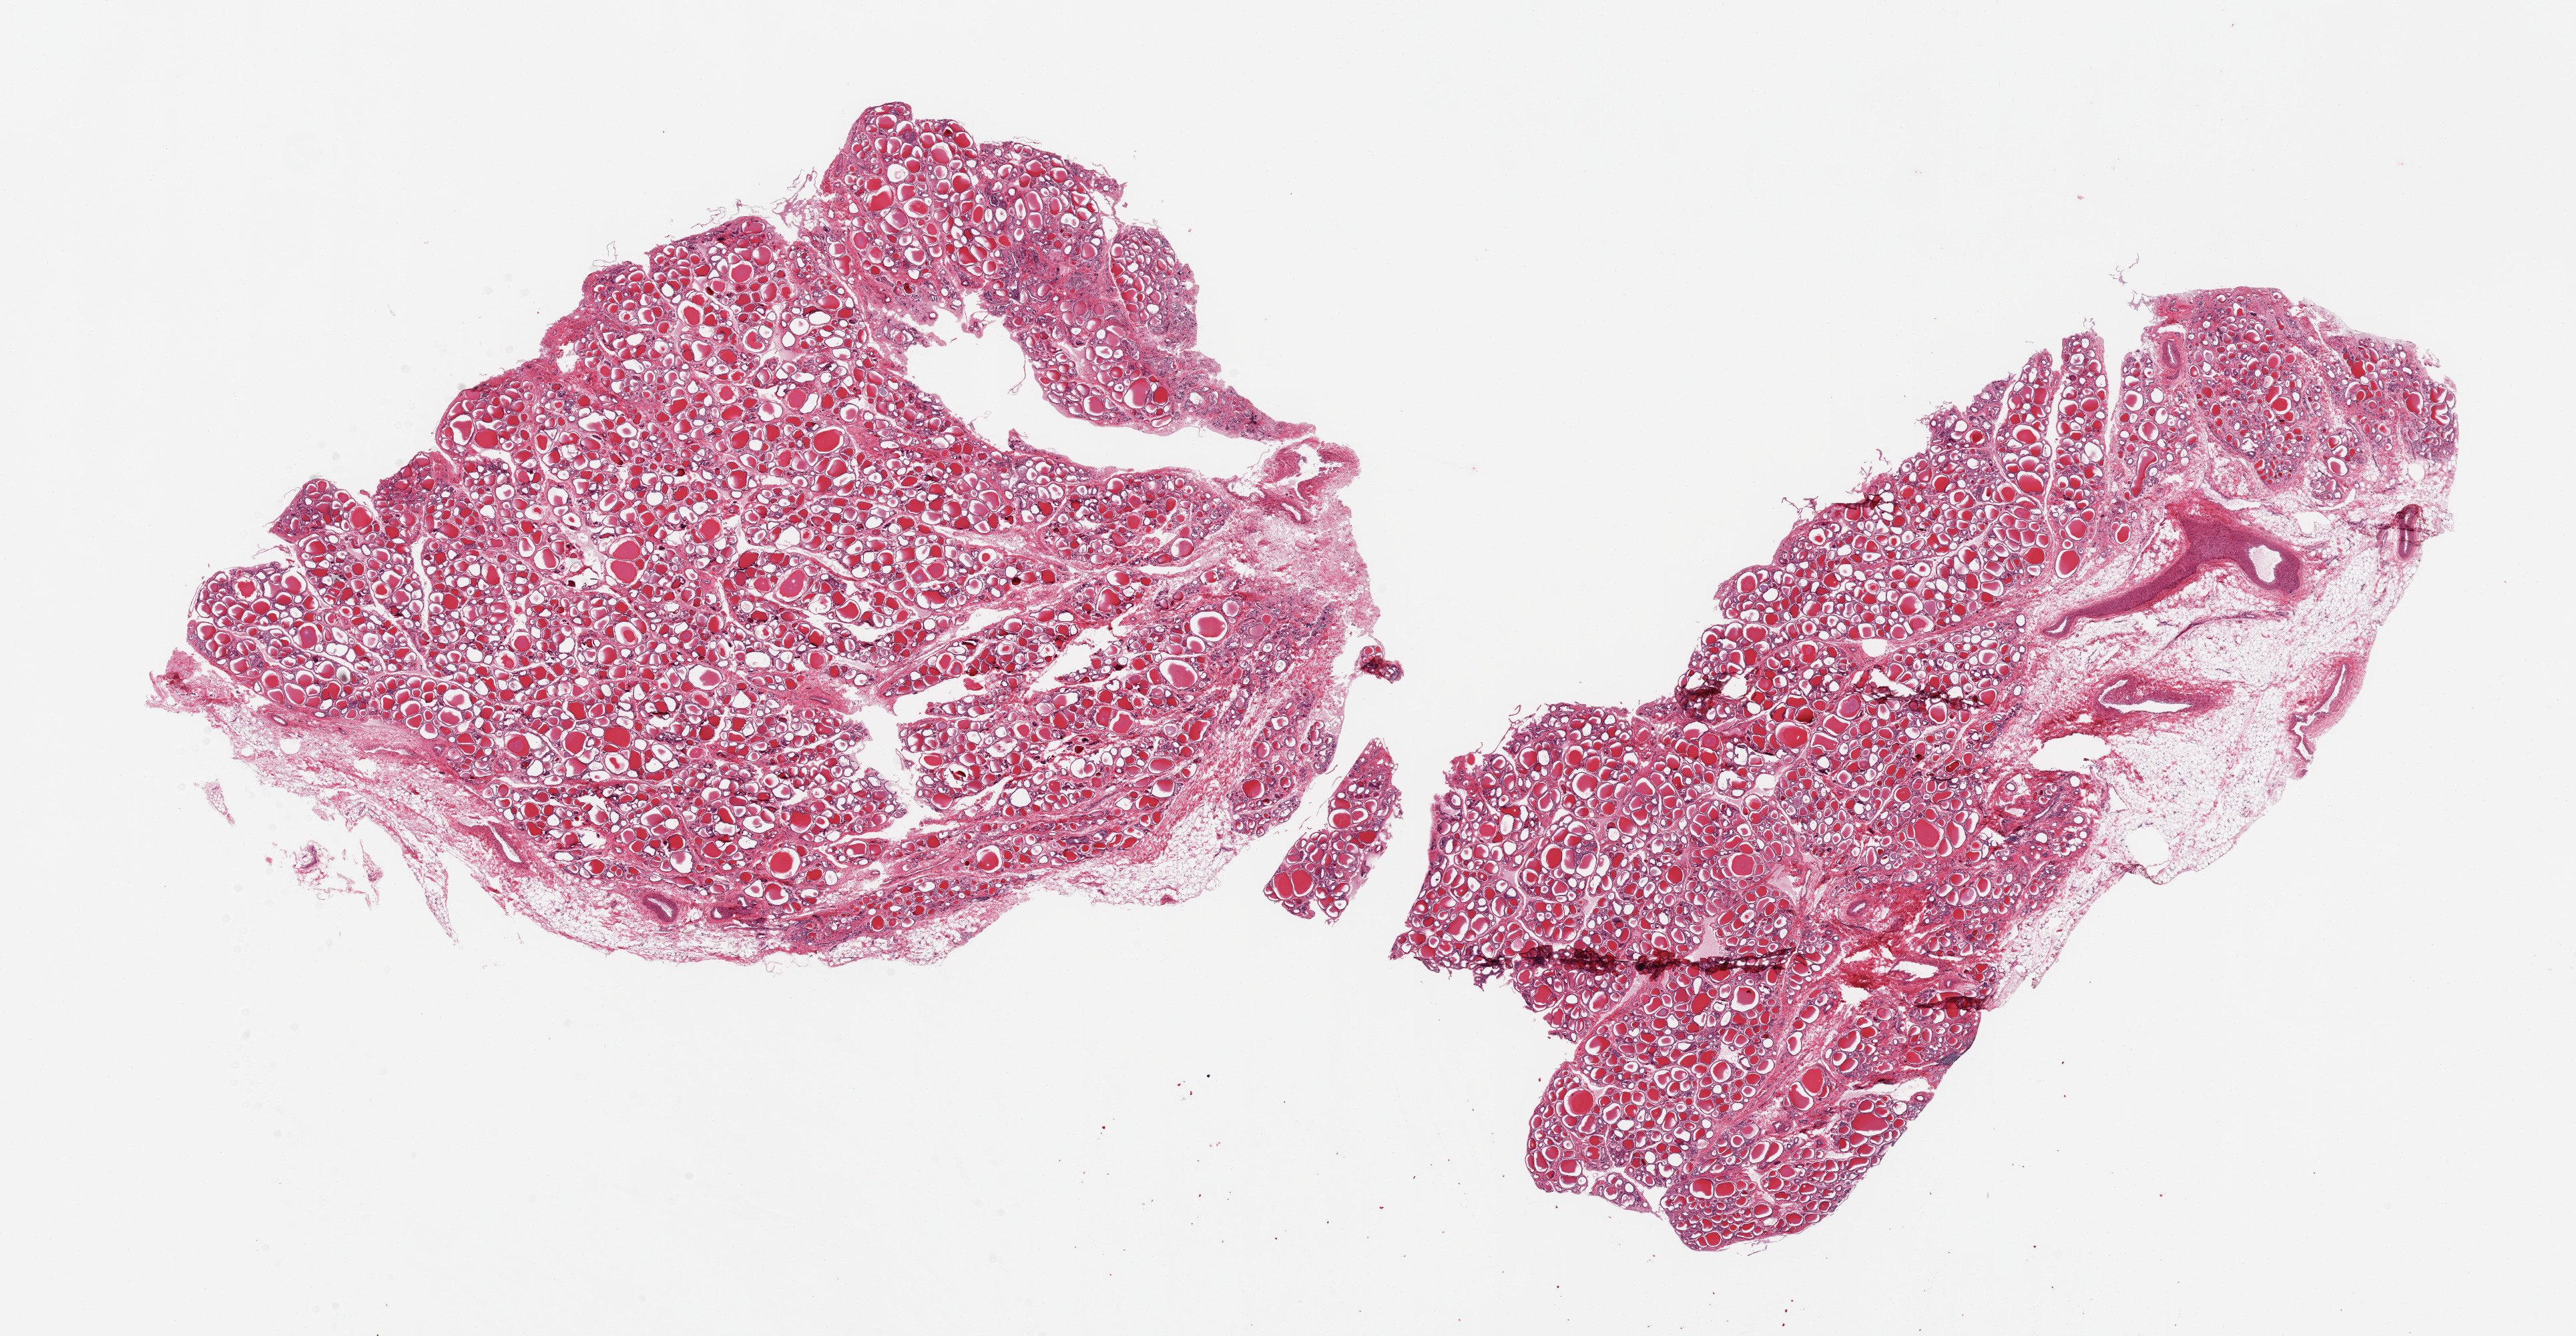
Digitized hematoxylin and eosin (H&E)-stained section, brightfield, shown as a low-resolution overview of the whole scanned area (about 30.5 x 15.8 mm, slide scanned at 20x); PAXgene-fixed paraffin-embedded (PFPE) section; sampled site (target tissue): thyroid; tissue donor sample. Donor: male.
Review note (as recorded): 2 pieces; 1 piece is ~20 fat/vessels, few collections of lymphocytes.